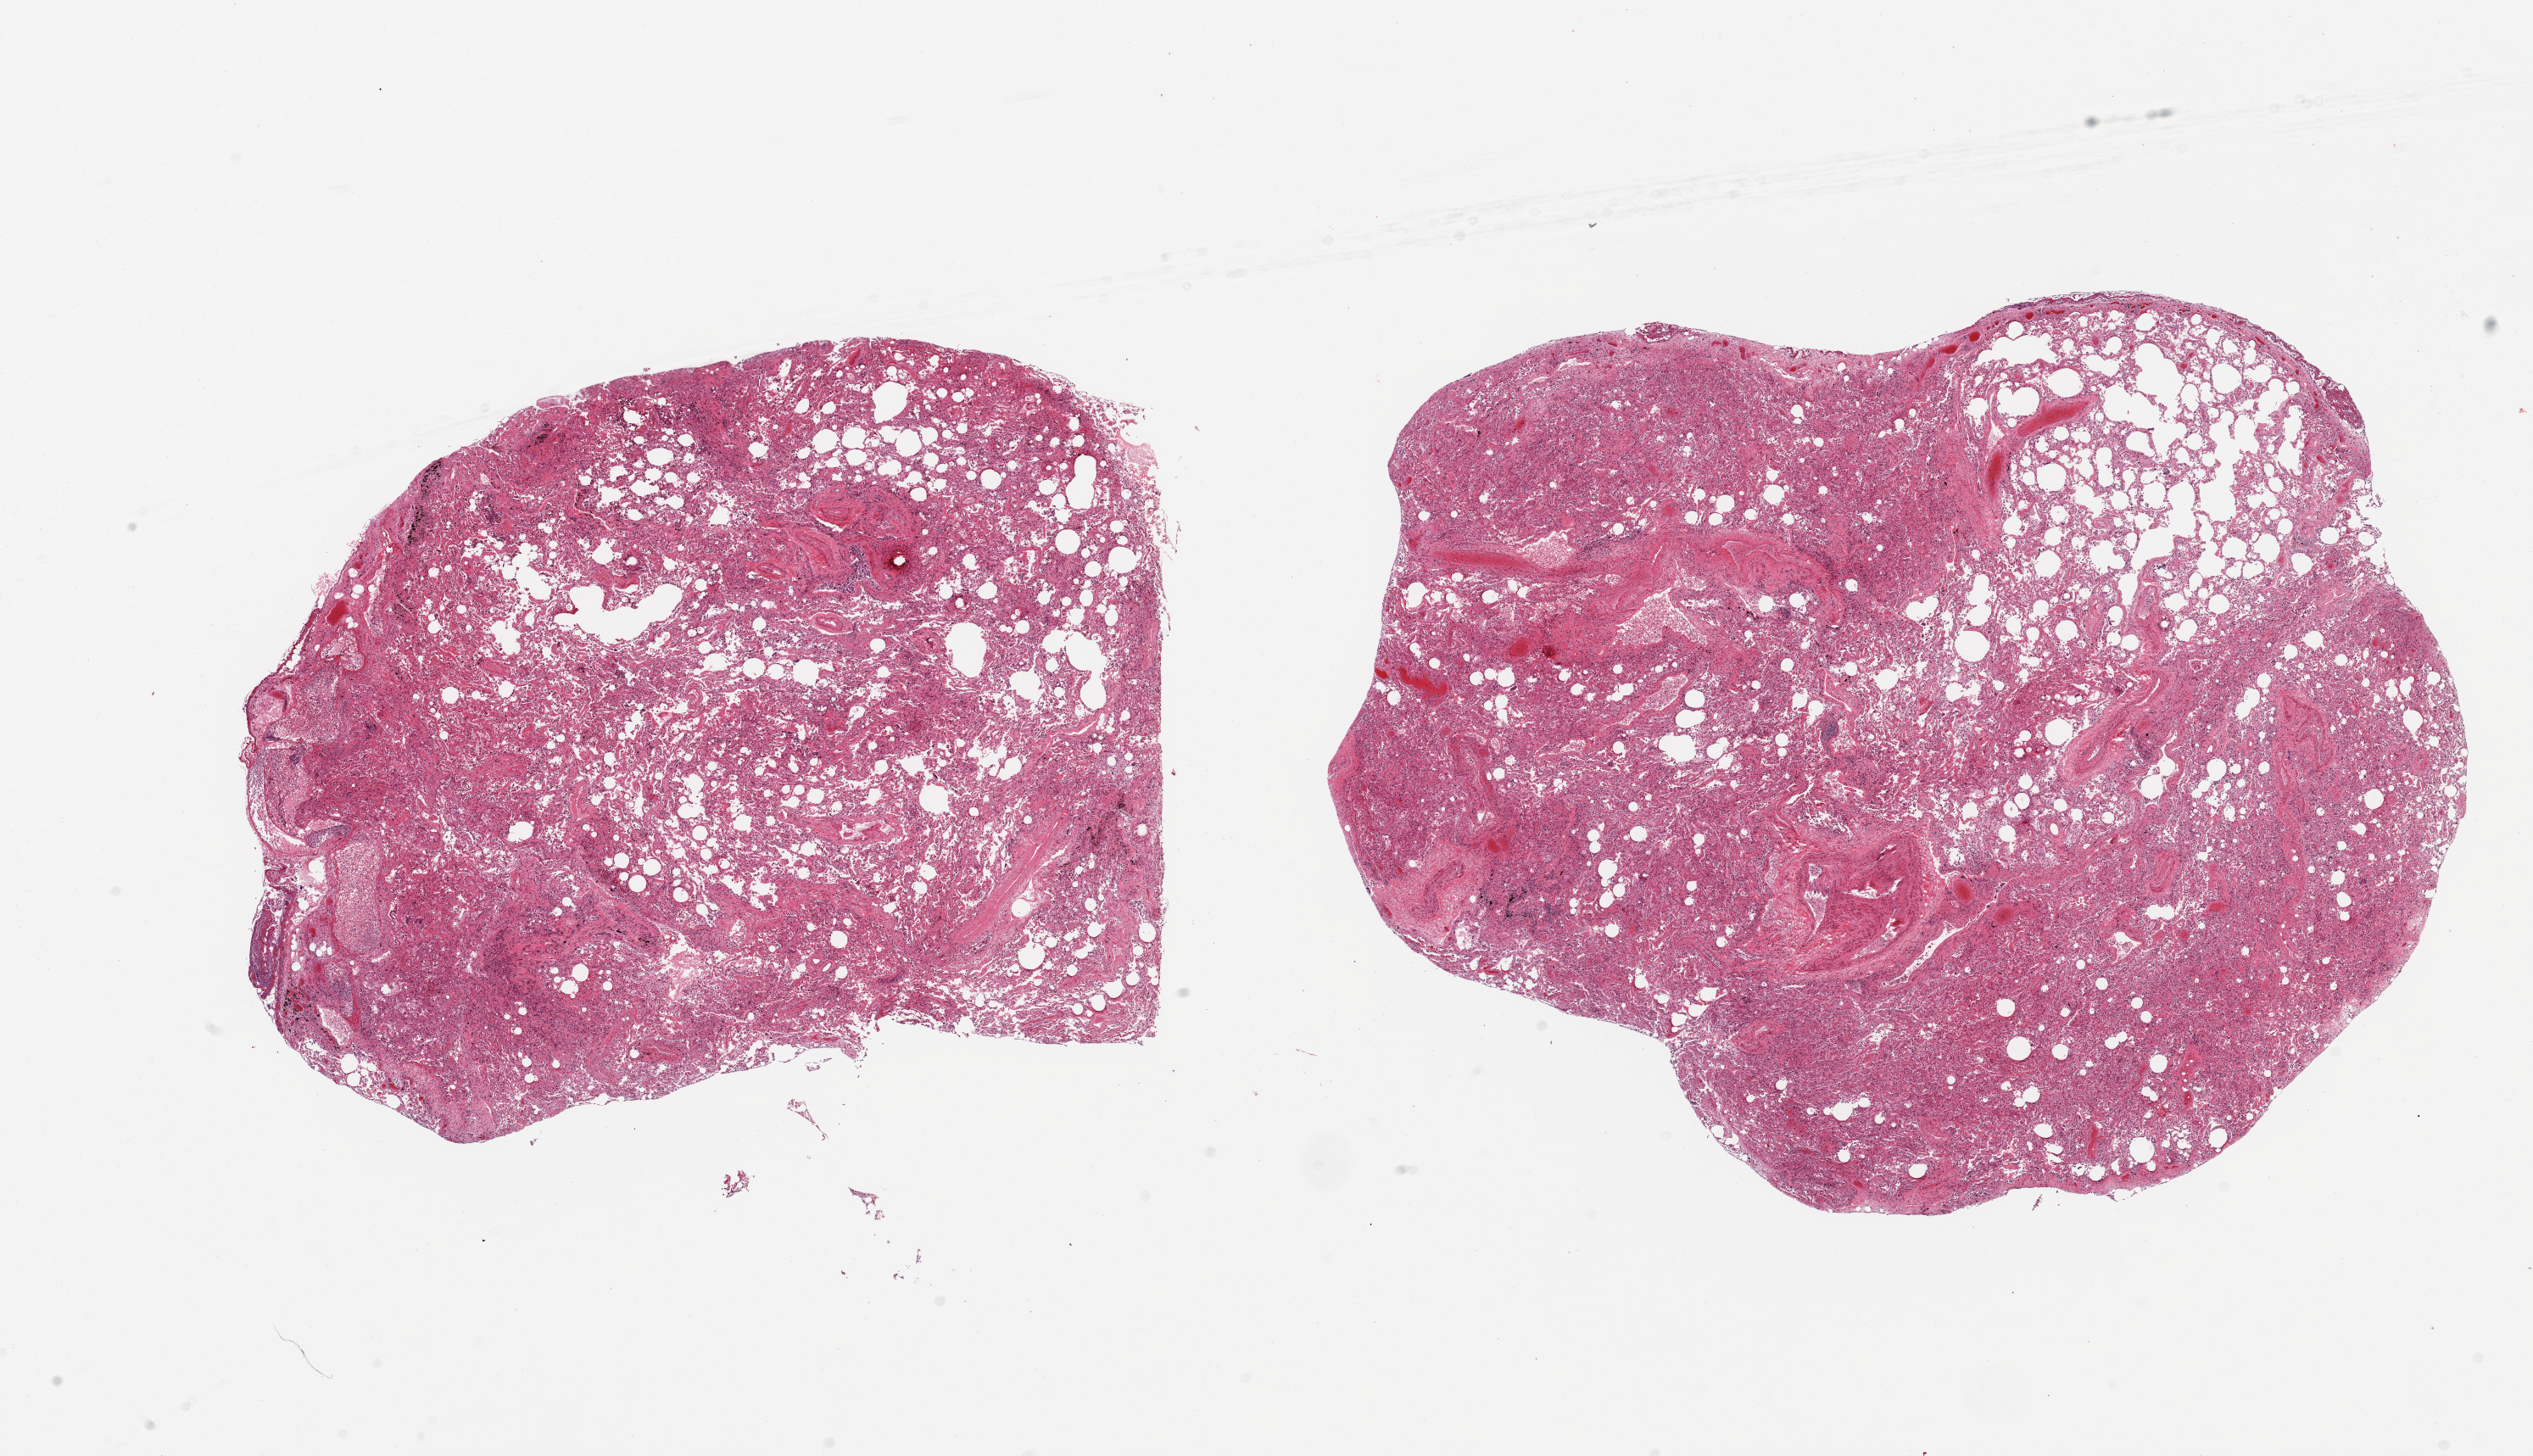
Haematoxylin and eosin whole-slide image, brightfield, low-resolution overview of the scanned area, about 23.6 x 13.6 mm; PAXgene-fixed, paraffin-embedded tissue; section of lung (target tissue); tissue donor sample. Male donor.
Review note (as recorded): 2 pieces; bronchopneumonia.